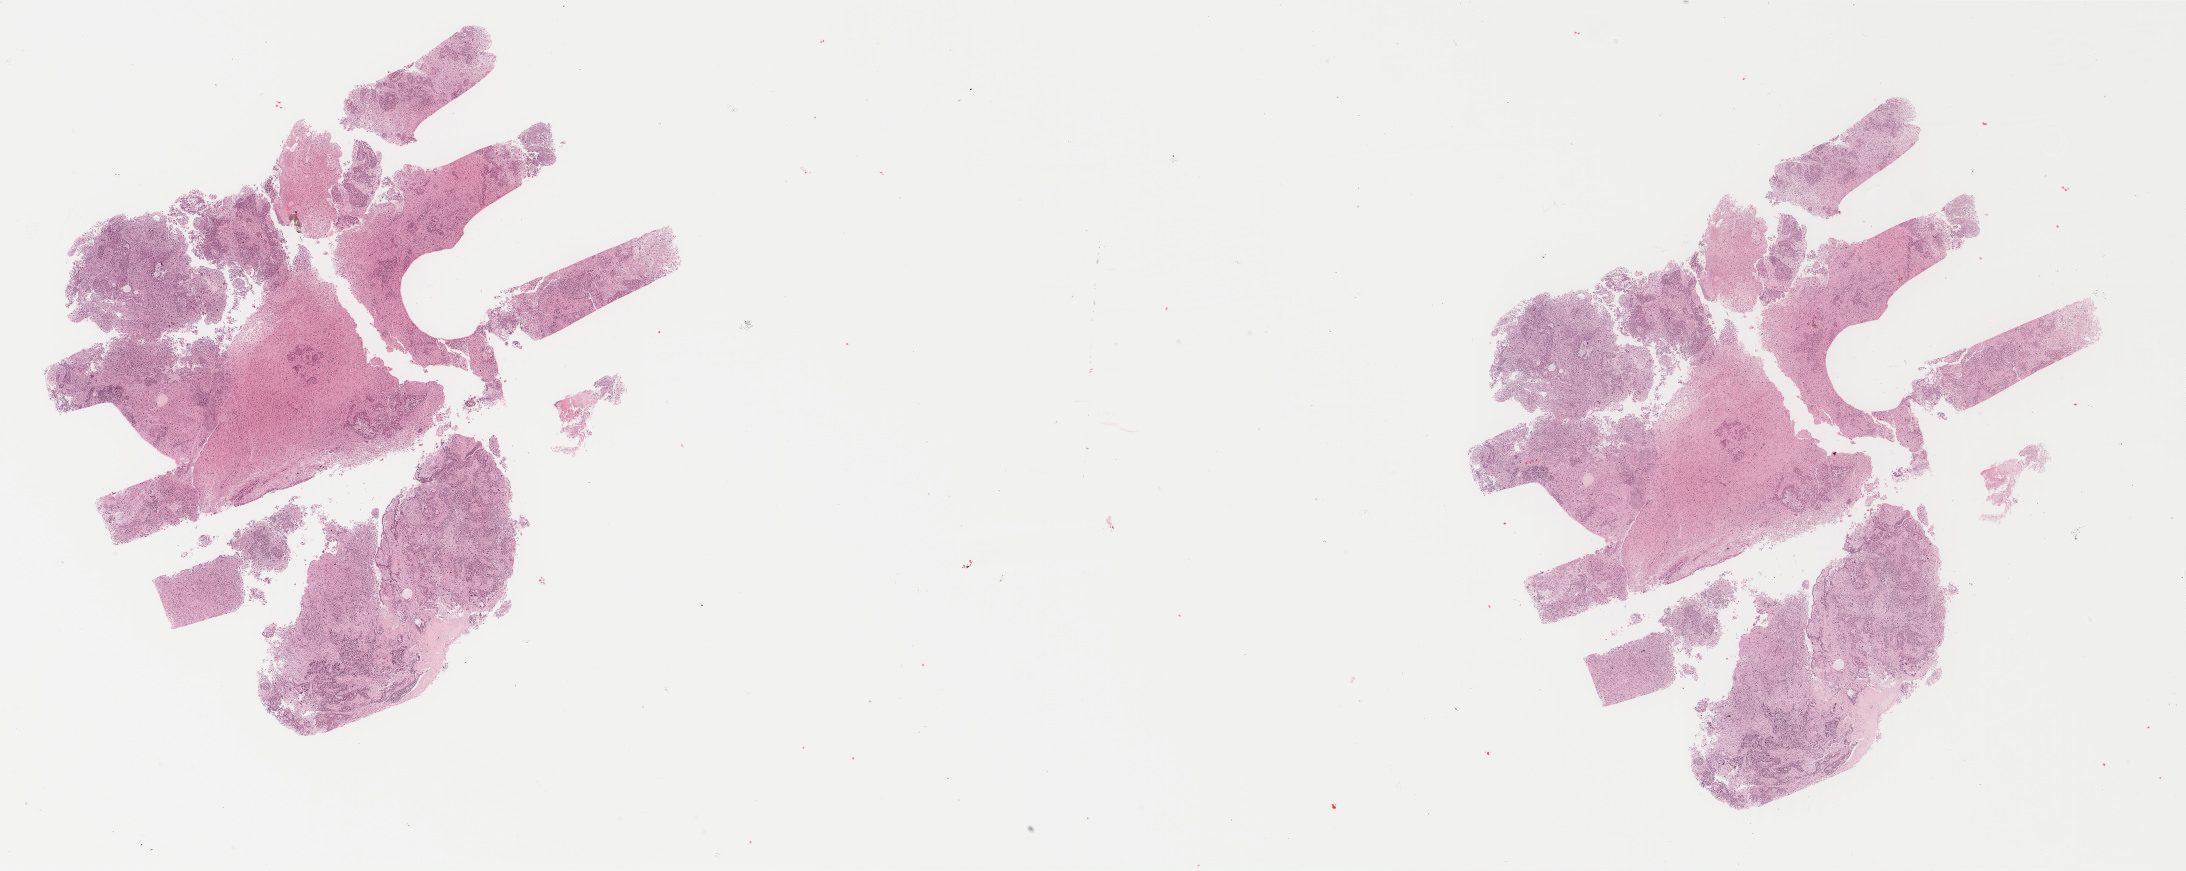
Whole-slide histology image, H&E-stained — a low-resolution overview of the entire scanned area, about 34.7 x 13.8 mm (slide scanned at 40x). Formalin-fixed paraffin-embedded (FFPE) diagnostic section. Sample: primary tumour, uterus. Female patient; age at initial diagnosis 68 years.
Diagnosis: Mullerian mixed tumor. FIGO stage: IA.